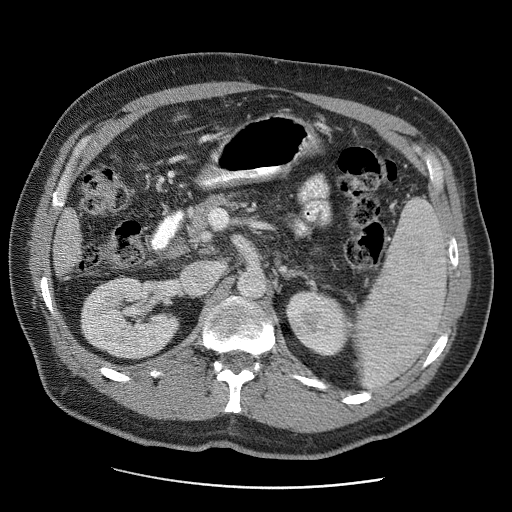
Contrast-enhanced abdominal CT (liver protocol), one axial slice. Slice 11 of 81 in the series (ordered by position). 120 kVp. Soft-tissue window (W 400 / L 40 HU). 2.5 mm slice thickness. 512 × 512 image matrix. Case-level facts recorded for this patient, not image findings: diagnosis: hepatocellular carcinoma (patient treated with transarterial chemoembolisation; whether this scan precedes or follows treatment is not stated here); TNM stage (as recorded): Stage-IIIA; Child-Pugh class: A; tumour nodularity: multinodular; tumour size: 5.5 cm.
Structures marked on this image (semi-automatically segmented with operator editing):
- liver parenchyma outside the tumour (the mass and vessels are separate outlines, so this box may not span the whole liver): bounding box <53,208,81,276> (left, top, right, bottom; pixels)